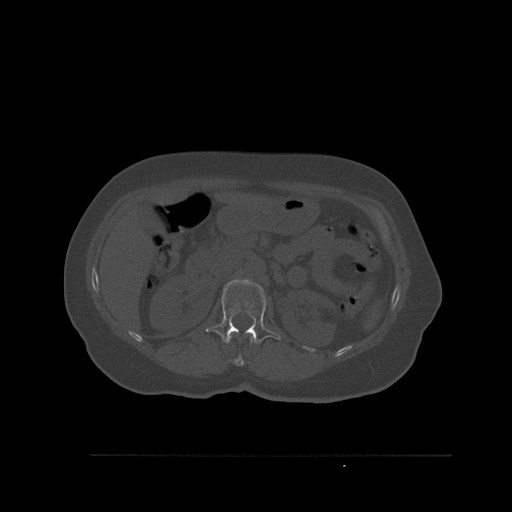
CT including the spine, one axial slice. Slice 267 of 527 in the series (ordered by position). Bone window (W 1800 / L 400 HU). 1.5 mm slice thickness. 512 × 512 image matrix. Patient: female, 73 years. From the clinical record (not read from this slice): primary cancer: breast.
Outlined on this slice (semi-automatic segmentation, software-assisted and operator-edited):
- L1 vertebra: bounding box <206,279,281,344> (left, top, right, bottom; pixels)
- T12 vertebra: <228,334,253,366>